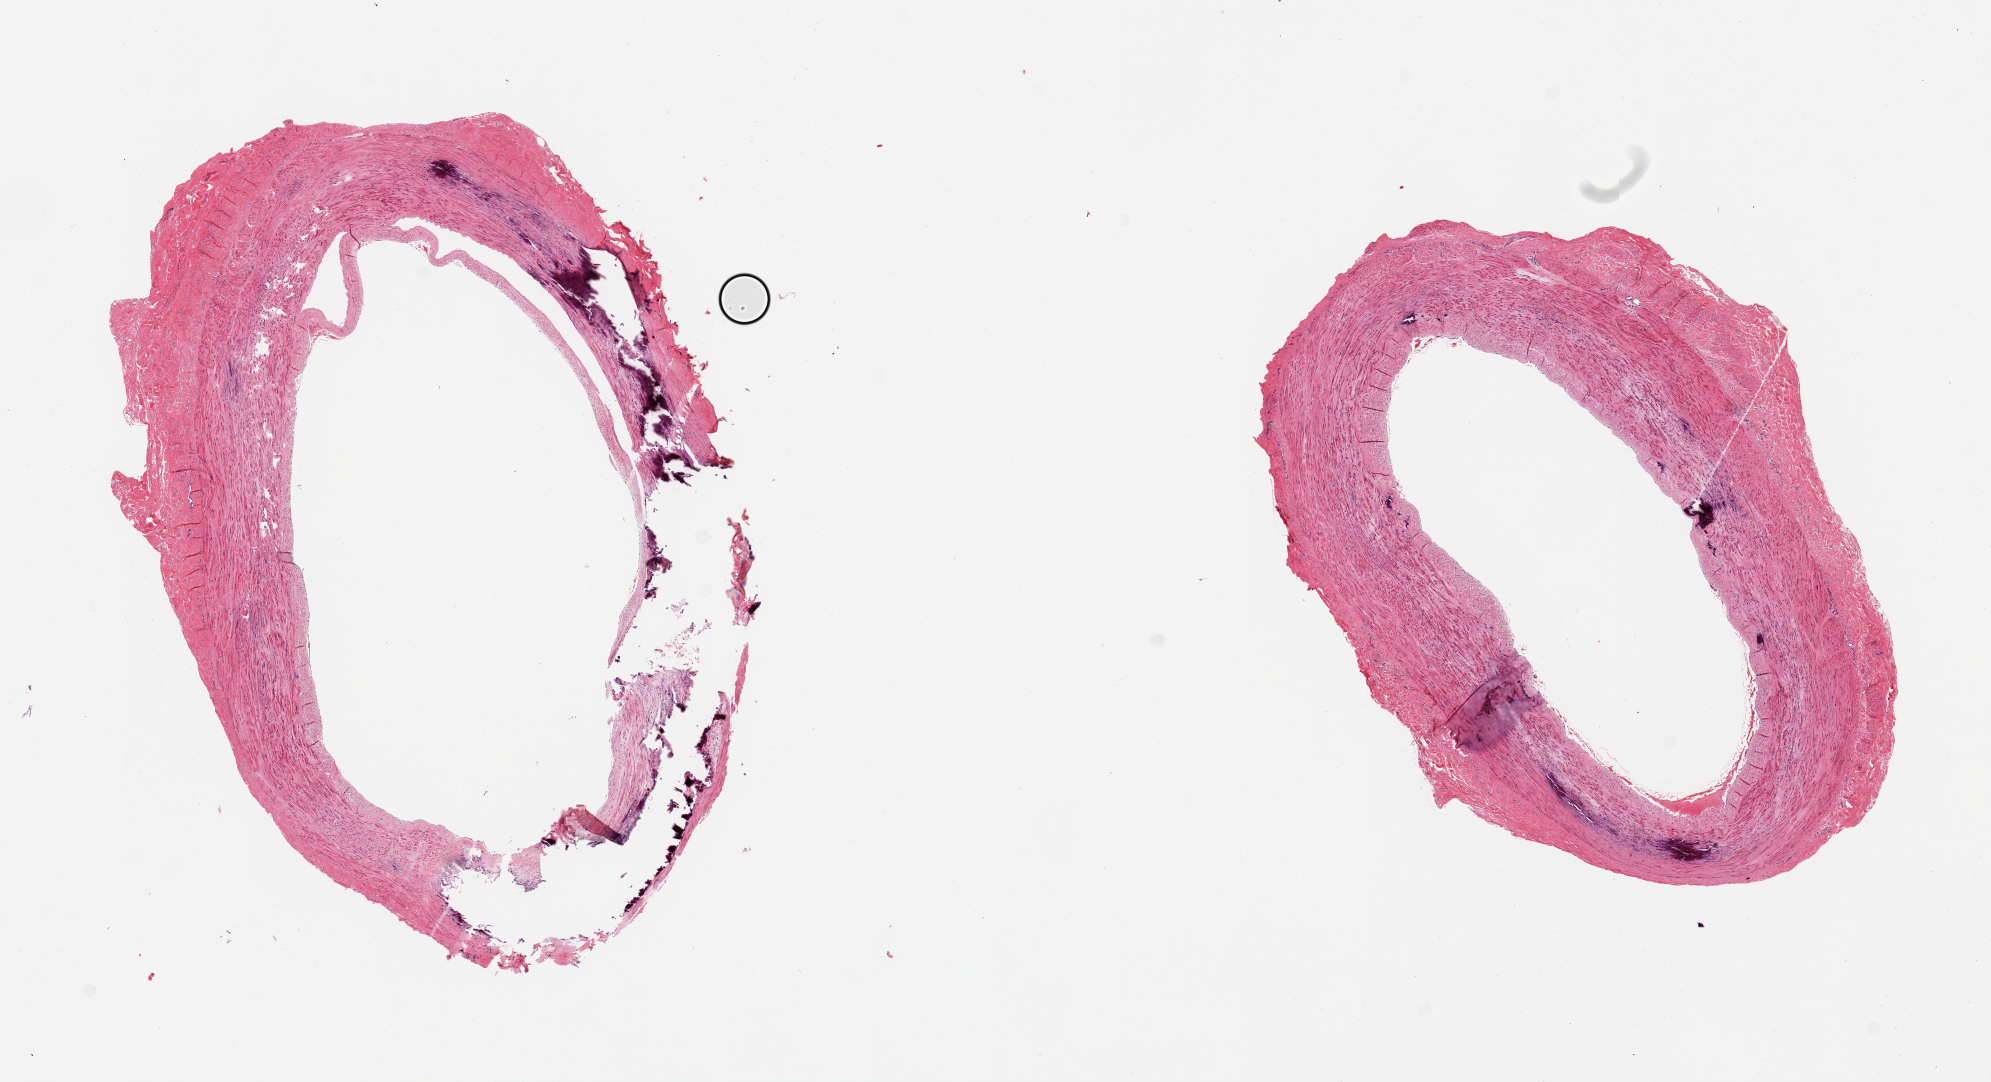
Digitized H&E-stained section, brightfield — low-resolution overview of the scanned area, about 15.8 x 8.6 mm. PAXgene-fixed, paraffin-embedded tissue. Sampled site (target tissue): tibial artery. Donor tissue sample. Male donor.
Reviewer comment on this tissue sample: 2 pieces; heavily calcified artery.